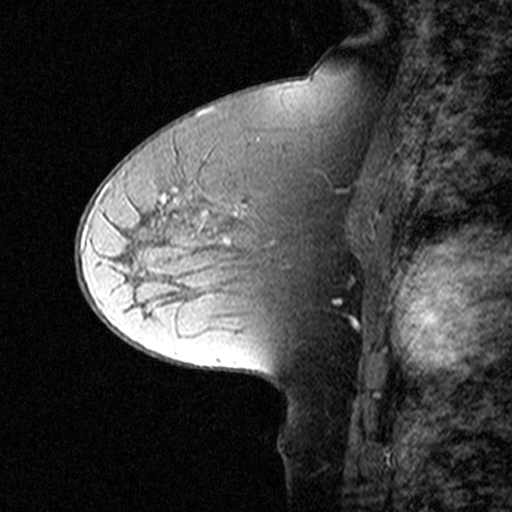
Breast MRI (dynamic contrast-enhanced), one sagittal slice. Dynamic contrast-enhanced study with each time point stored as its own series, time point 2 of 3 at this slice position (early post-contrast, ordered by acquisition time). 1.5 T. TE 4.5 ms, TR 11 ms. 512 × 512 image matrix, field of view 200 × 200 mm. Female patient, age 50 years. From the clinical record (not read from this slice): setting: breast cancer imaged before/during neoadjuvant chemotherapy; receptor status: HR-positive, HER2-negative.
Annotated regions visible in this slice (semi-automatic segmentation, software-assisted and operator-edited):
- analysis volume of interest (the breast-tissue region the enhancement analysis was run in; not a lesion): bounding box <126,162,329,291> (left, top, right, bottom; pixels)
- tumour enhancement mask (voxels above the 90 % enhancement threshold inside the analysis volume of interest): <160,194,249,217>